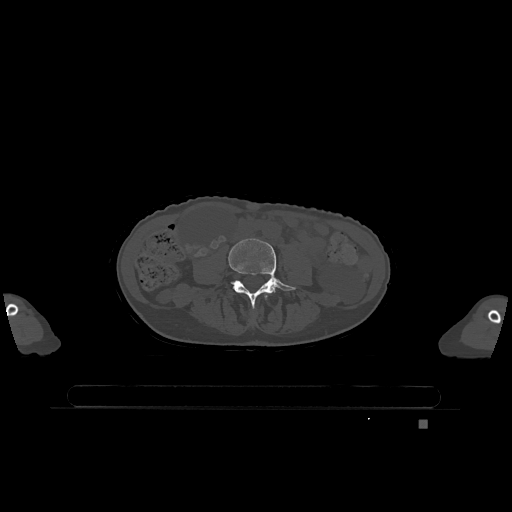
CT including the spine, one axial slice; position 297 of 1317 along the scan axis; bone window (W 1800 / L 400 HU); 512 × 512 image matrix. Patient: female, 74 years. From the clinical record (not read from this slice): primary cancer: lung; vertebrae with lytic lesions (as recorded): T1, T4, T5, T6, L4, L5.
Outlined on this slice (semi-automatic segmentation, software-assisted and operator-edited):
- L3 vertebra: bounding box <264,293,270,300> (left, top, right, bottom; pixels)
- L4 vertebra: <229,238,296,307>